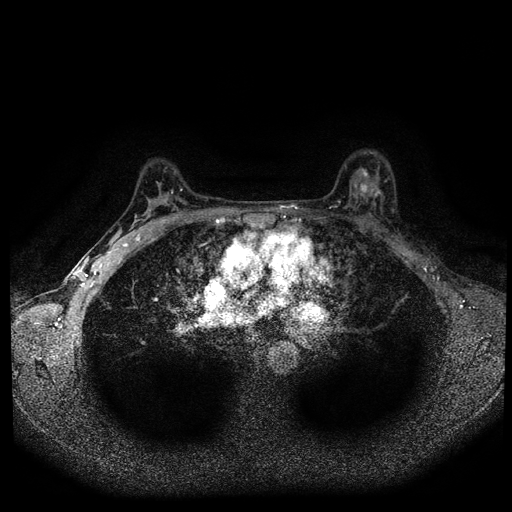
Breast MRI (dynamic contrast-enhanced, multi-phase), one axial slice; slice 62 of 108 in the series (ordered by position); dynamic contrast-enhanced series, time point 2 of 5 at this slice position (early post-contrast); 1.5 T; TE 2.7 ms, TR 5.5 ms; 2 mm slice thickness; 512 × 512 image matrix. Patient: female, 36 years.
Annotated regions visible in this slice (semi-automatic segmentation, software-assisted and operator-edited):
- breast lesion (labelled 'tumour' in the annotation; benign lesions carry a separate 'benign' label): bounding box [x1, y1, x2, y2] px = [350, 166, 374, 201]